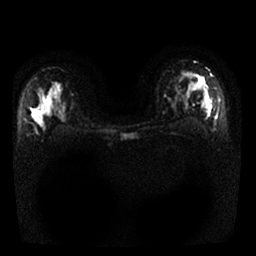
Breast MRI, one axial slice. Slice 19 of 25 in the series (ordered by position). Diffusion-weighted series; image 2 of 4 stored at this slice position (different b-values; order by instance number). 1.5 T. 4 mm slice thickness. 256 × 256 image matrix, field of view 320 × 320 mm. Female patient.
Structures marked on this image (expert manual segmentation):
- tumour on diffusion-weighted imaging: box from (x=193, y=72) to (x=209, y=94) px